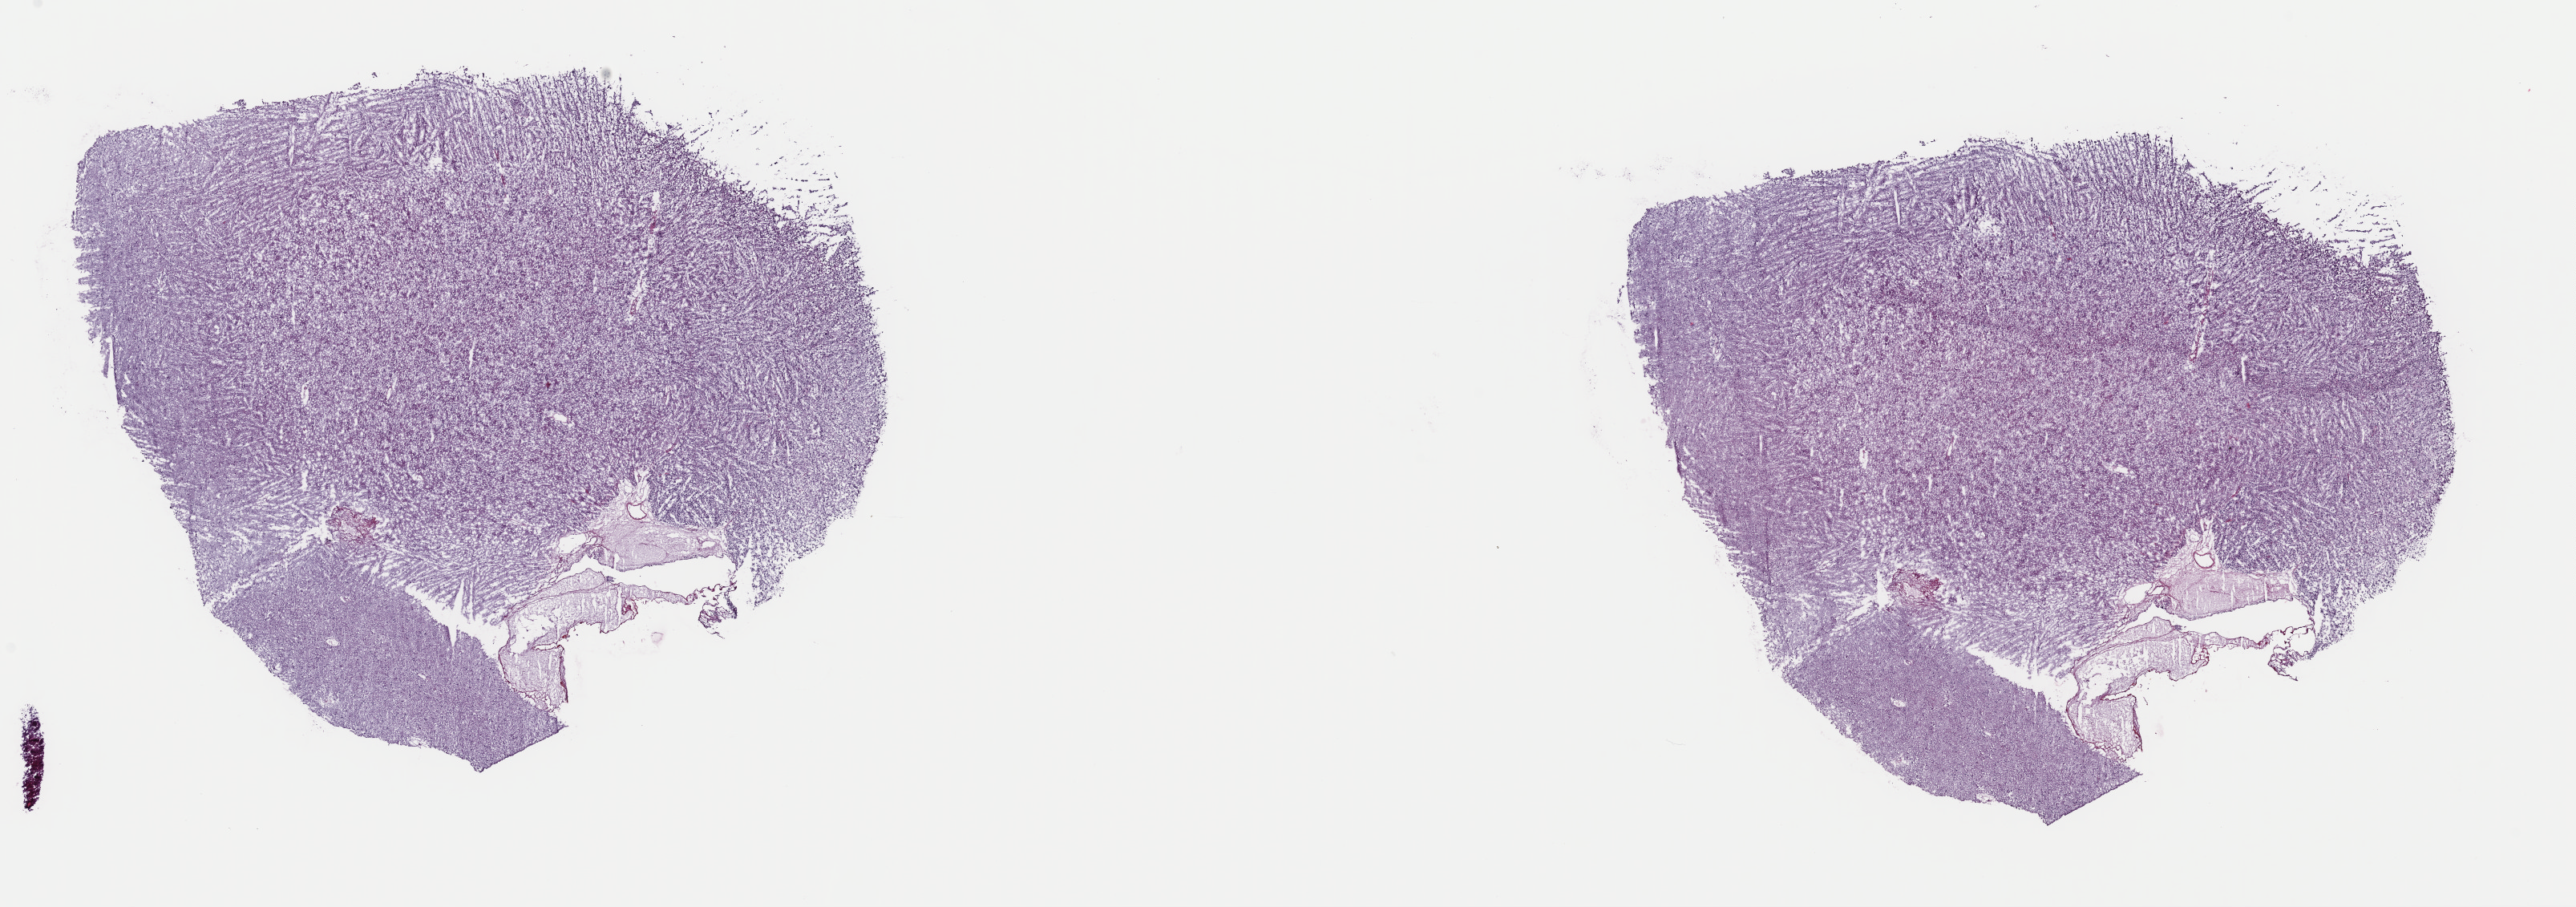
Digitized Hematoxylin and eosin (H&E) stained tissue section (whole slide), low-resolution overview of the scanned area, about 25.4 x 8.9 mm (slide scanned at 40x). Frozen section. Primary tumour sample from the brain. Patient: female, age at initial diagnosis 65 years. Histologic grade: G3 (poorly differentiated). Pathologist review of this section (percent, as recorded): tumour cells 75%, tumour nuclei 80%, normal cells 10%, stromal cells 5%, necrosis 10%. Inflammatory infiltration, as recorded: lymphocyte infiltration 0%, monocyte infiltration 0%, neutrophil infiltration 0%.
• diagnosis: Mixed glioma (cerebrum)
• laterality: right